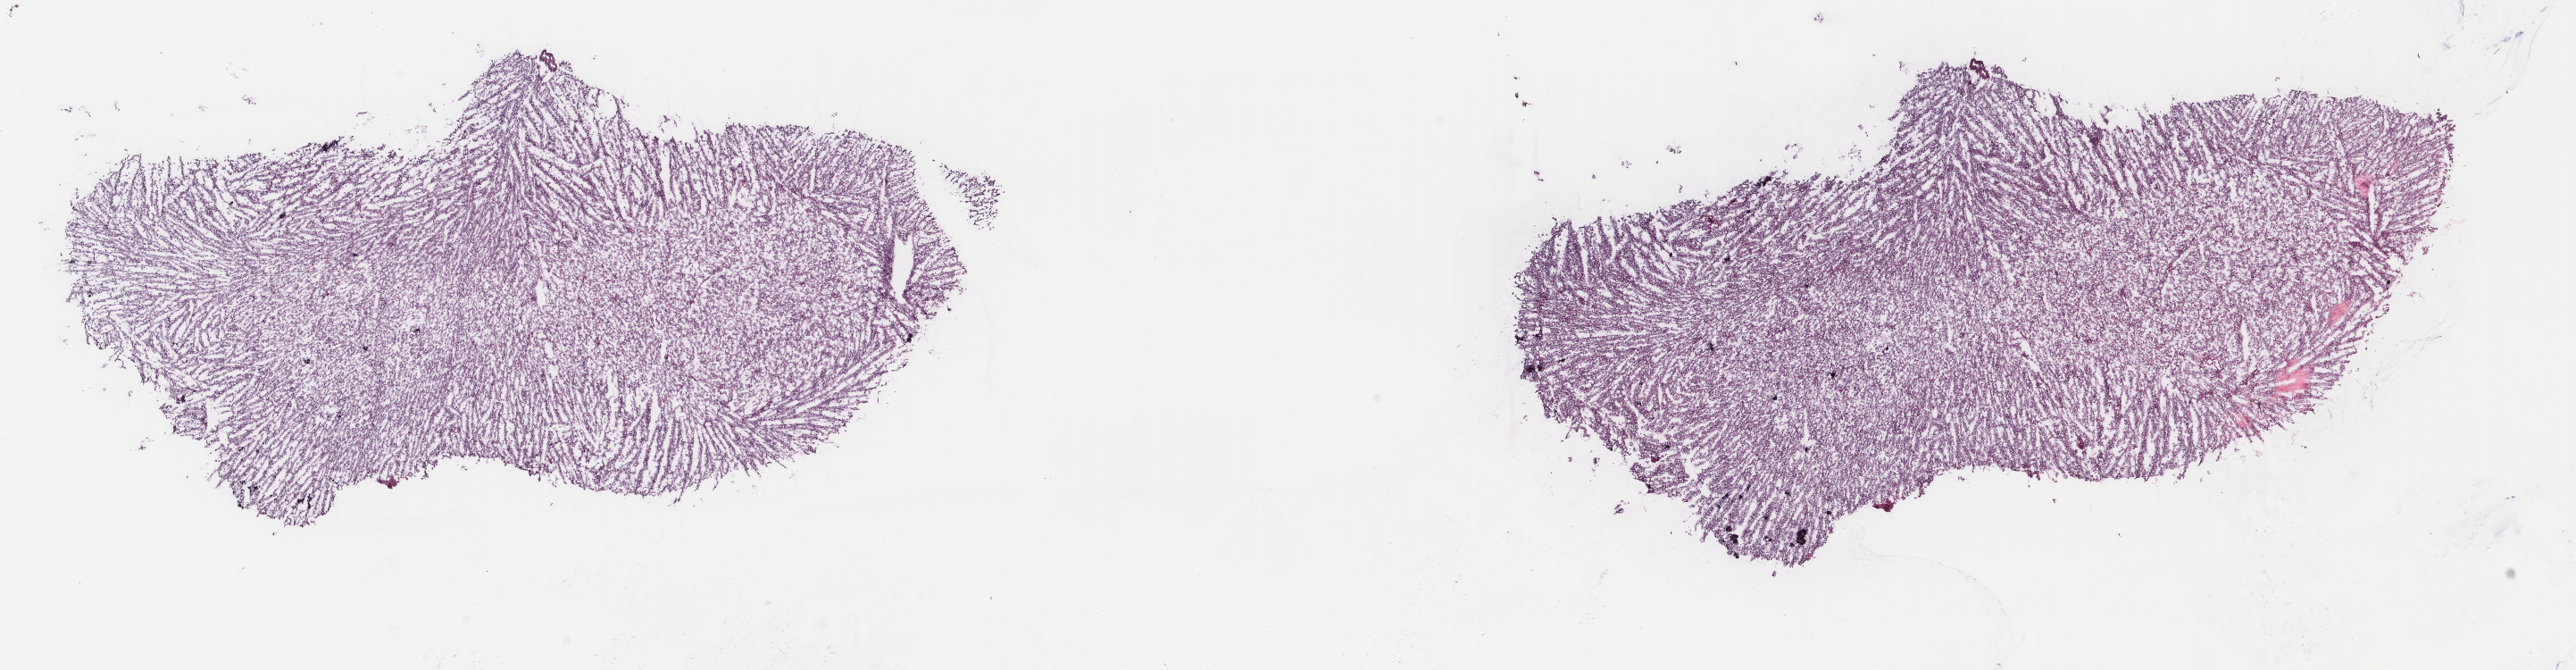
Hematoxylin and eosin (H&E) stained whole-slide image, low-resolution overview of the scanned area, about 22.9 x 6.0 mm. Frozen section from the top of the tissue portion. Brain, primary tumour sample. Patient: female, age at initial diagnosis 28 years. Slide review estimates, as recorded: tumour cells 80%, tumour nuclei 85%.
Histologic diagnosis: Mixed glioma (cerebrum).